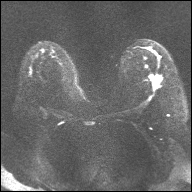
Breast MRI, one axial slice. Slice 19 of 32 in the series (ordered by position). Diffusion-weighted series; image 2 of 4 stored at this slice position (different b-values; order by instance number). 1.5 T. 4 mm slice thickness. 192 × 192 image matrix, field of view 360 × 360 mm. Female patient.
Structures marked on this image (outlined manually by an expert reader):
- tumour on diffusion-weighted imaging: bounding box [x1, y1, x2, y2] px = [153, 76, 160, 83]